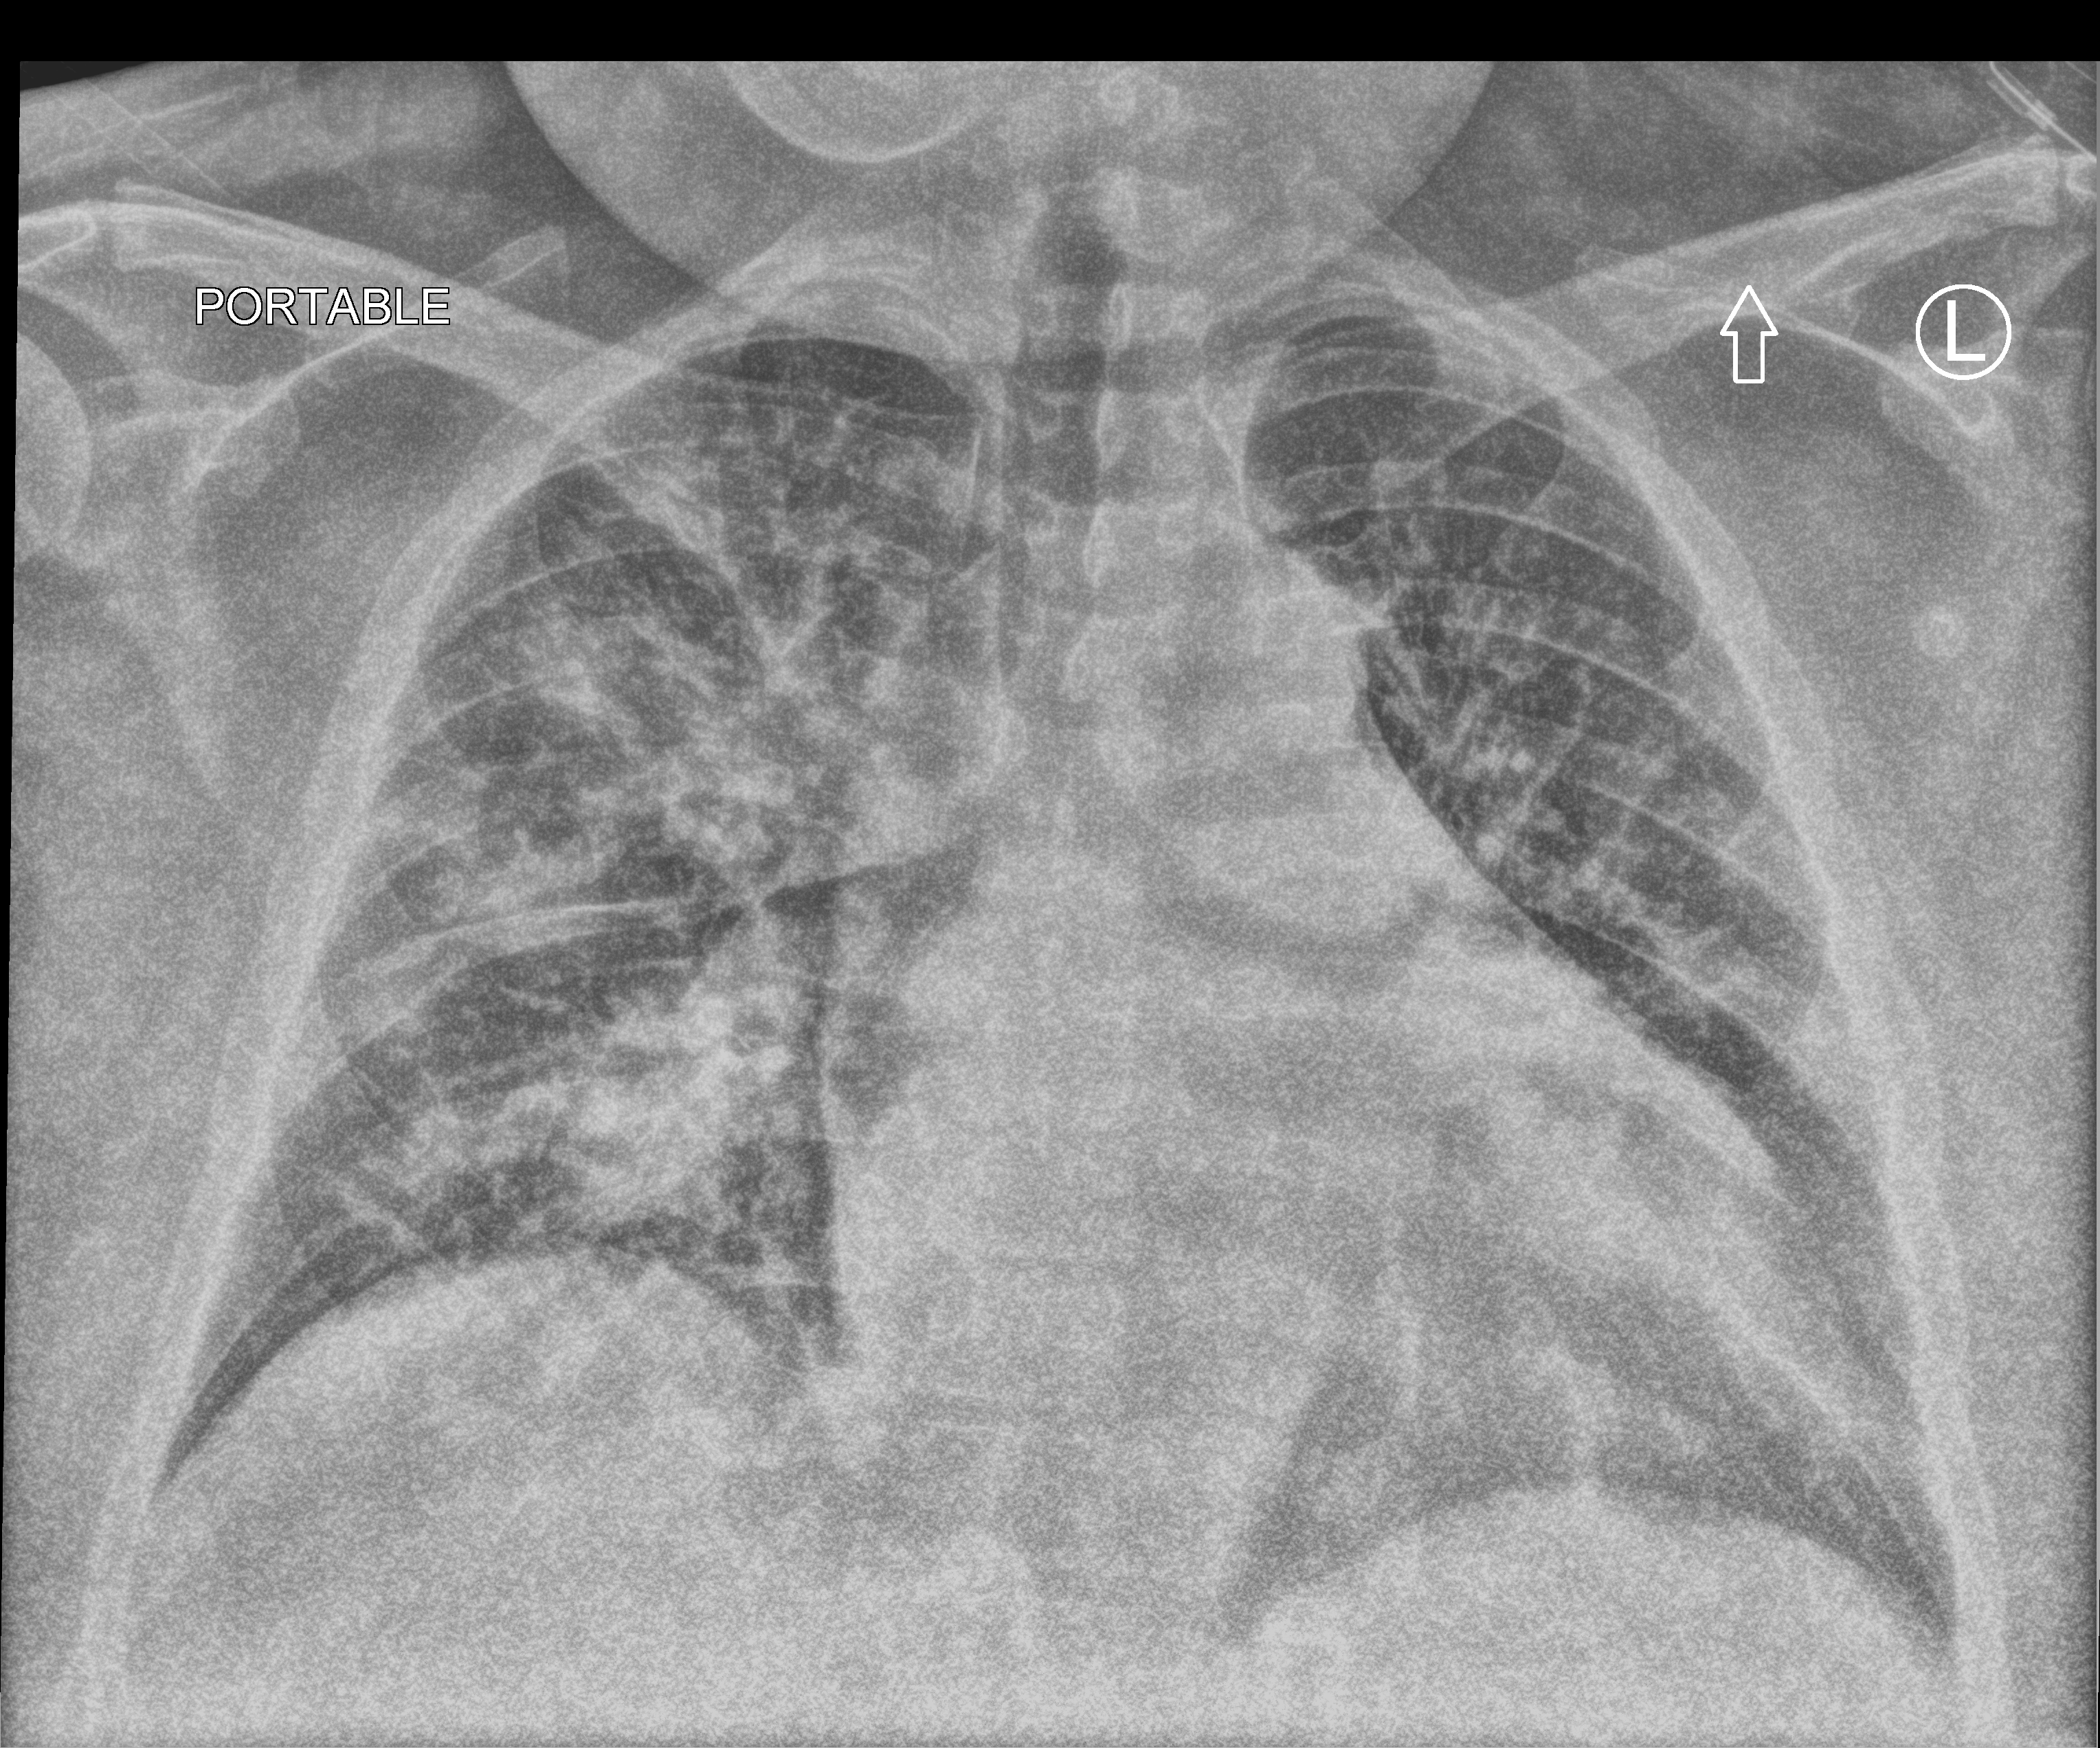
Chest X-ray (portable); anteroposterior (AP) projection. Male patient hospitalised with COVID-19, age 18–59 years.
From the hospital-stay record, not from the radiograph (when in the stay this image was taken is not recorded): length of hospital stay: 20 days; mechanically ventilated during this hospital stay: no; other chronic lung disease (admission record): no.